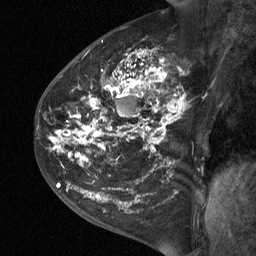
Breast MRI (dynamic contrast-enhanced), one sagittal slice. Position 34 of 64 along the scan axis. Dynamic contrast-enhanced study with each time point stored as its own series, time point 2 of 3 at this slice position (early post-contrast, ordered by acquisition time). 1.5 T. TE 4.8 ms, TR 27 ms. 256 × 256 image matrix, field of view 200 × 200 mm. Patient: female, 42 years. Case-level facts recorded for this patient, not image findings: setting: breast cancer imaged before/during neoadjuvant chemotherapy; receptor status: triple-negative.
Annotated regions visible in this slice (semi-automatically segmented with operator editing):
- analysis volume of interest (the breast-tissue region the enhancement analysis was run in; not a lesion): box from (x=43, y=29) to (x=203, y=190) px
- tumour enhancement mask (voxels above the 90 % enhancement threshold inside the analysis volume of interest): (x=54, y=50)–(x=185, y=160)